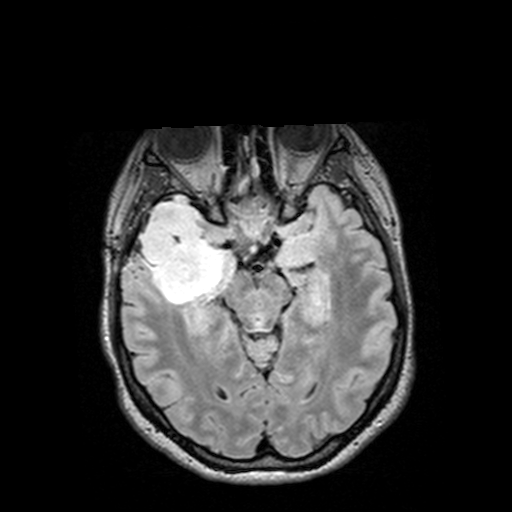
Brain MRI from a brain-tumour surgery series, one axial slice; slice 86 of 144 in the series (ordered by position); T2 FLAIR; 512 × 512 image matrix. From the clinical record (not read from this slice): histopathology: Astrocytoma; WHO grade: 3; IDH mutation: yes.
Structures marked on this image (expert manual segmentation):
- tumour: bounding box <126,195,232,305> (left, top, right, bottom; pixels)